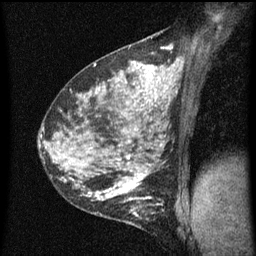
Breast MRI (dynamic contrast-enhanced), one sagittal slice; position 34 of 60 along the scan axis; dynamic contrast-enhanced series, image 2 of 5 at this slice position (ordered by acquisition); 1.5 T; TE 4.2 ms, TR 8 ms; 2 mm slice thickness; 256 × 256 image matrix, field of view 180 × 180 mm. Female patient, age 35 years.
Outlined on this slice (semi-automatically segmented with operator editing):
- analysis volume of interest (the breast-tissue region the enhancement analysis was run in; not a lesion): box from (x=118, y=190) to (x=165, y=229) px
- tumour enhancement mask (voxels above the 70 % enhancement threshold inside the analysis volume of interest): (x=118, y=190)–(x=159, y=217)